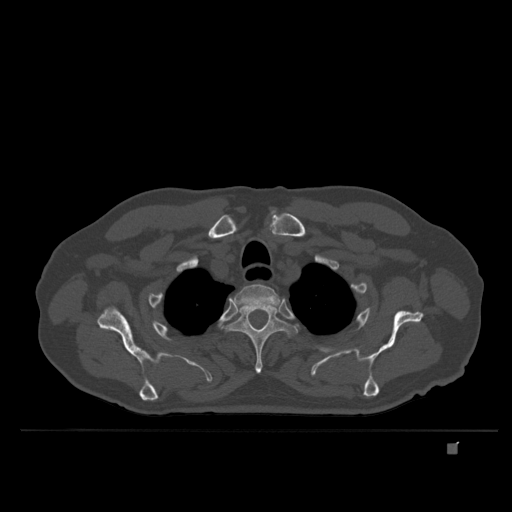
CT including the spine, one axial slice; position 303 of 435 along the scan axis; bone window (W 1800 / L 400 HU); 1.5 mm slice thickness; 512 × 512 image matrix, field of view 434 × 434 mm. Patient: male, 73 years. From the clinical record (not read from this slice): primary cancer: skin.
Structures marked on this image (semi-automatic segmentation, software-assisted and operator-edited):
- T2 vertebra: bounding box <231,284,279,311> (left, top, right, bottom; pixels)
- T3 vertebra: <226,301,297,374>